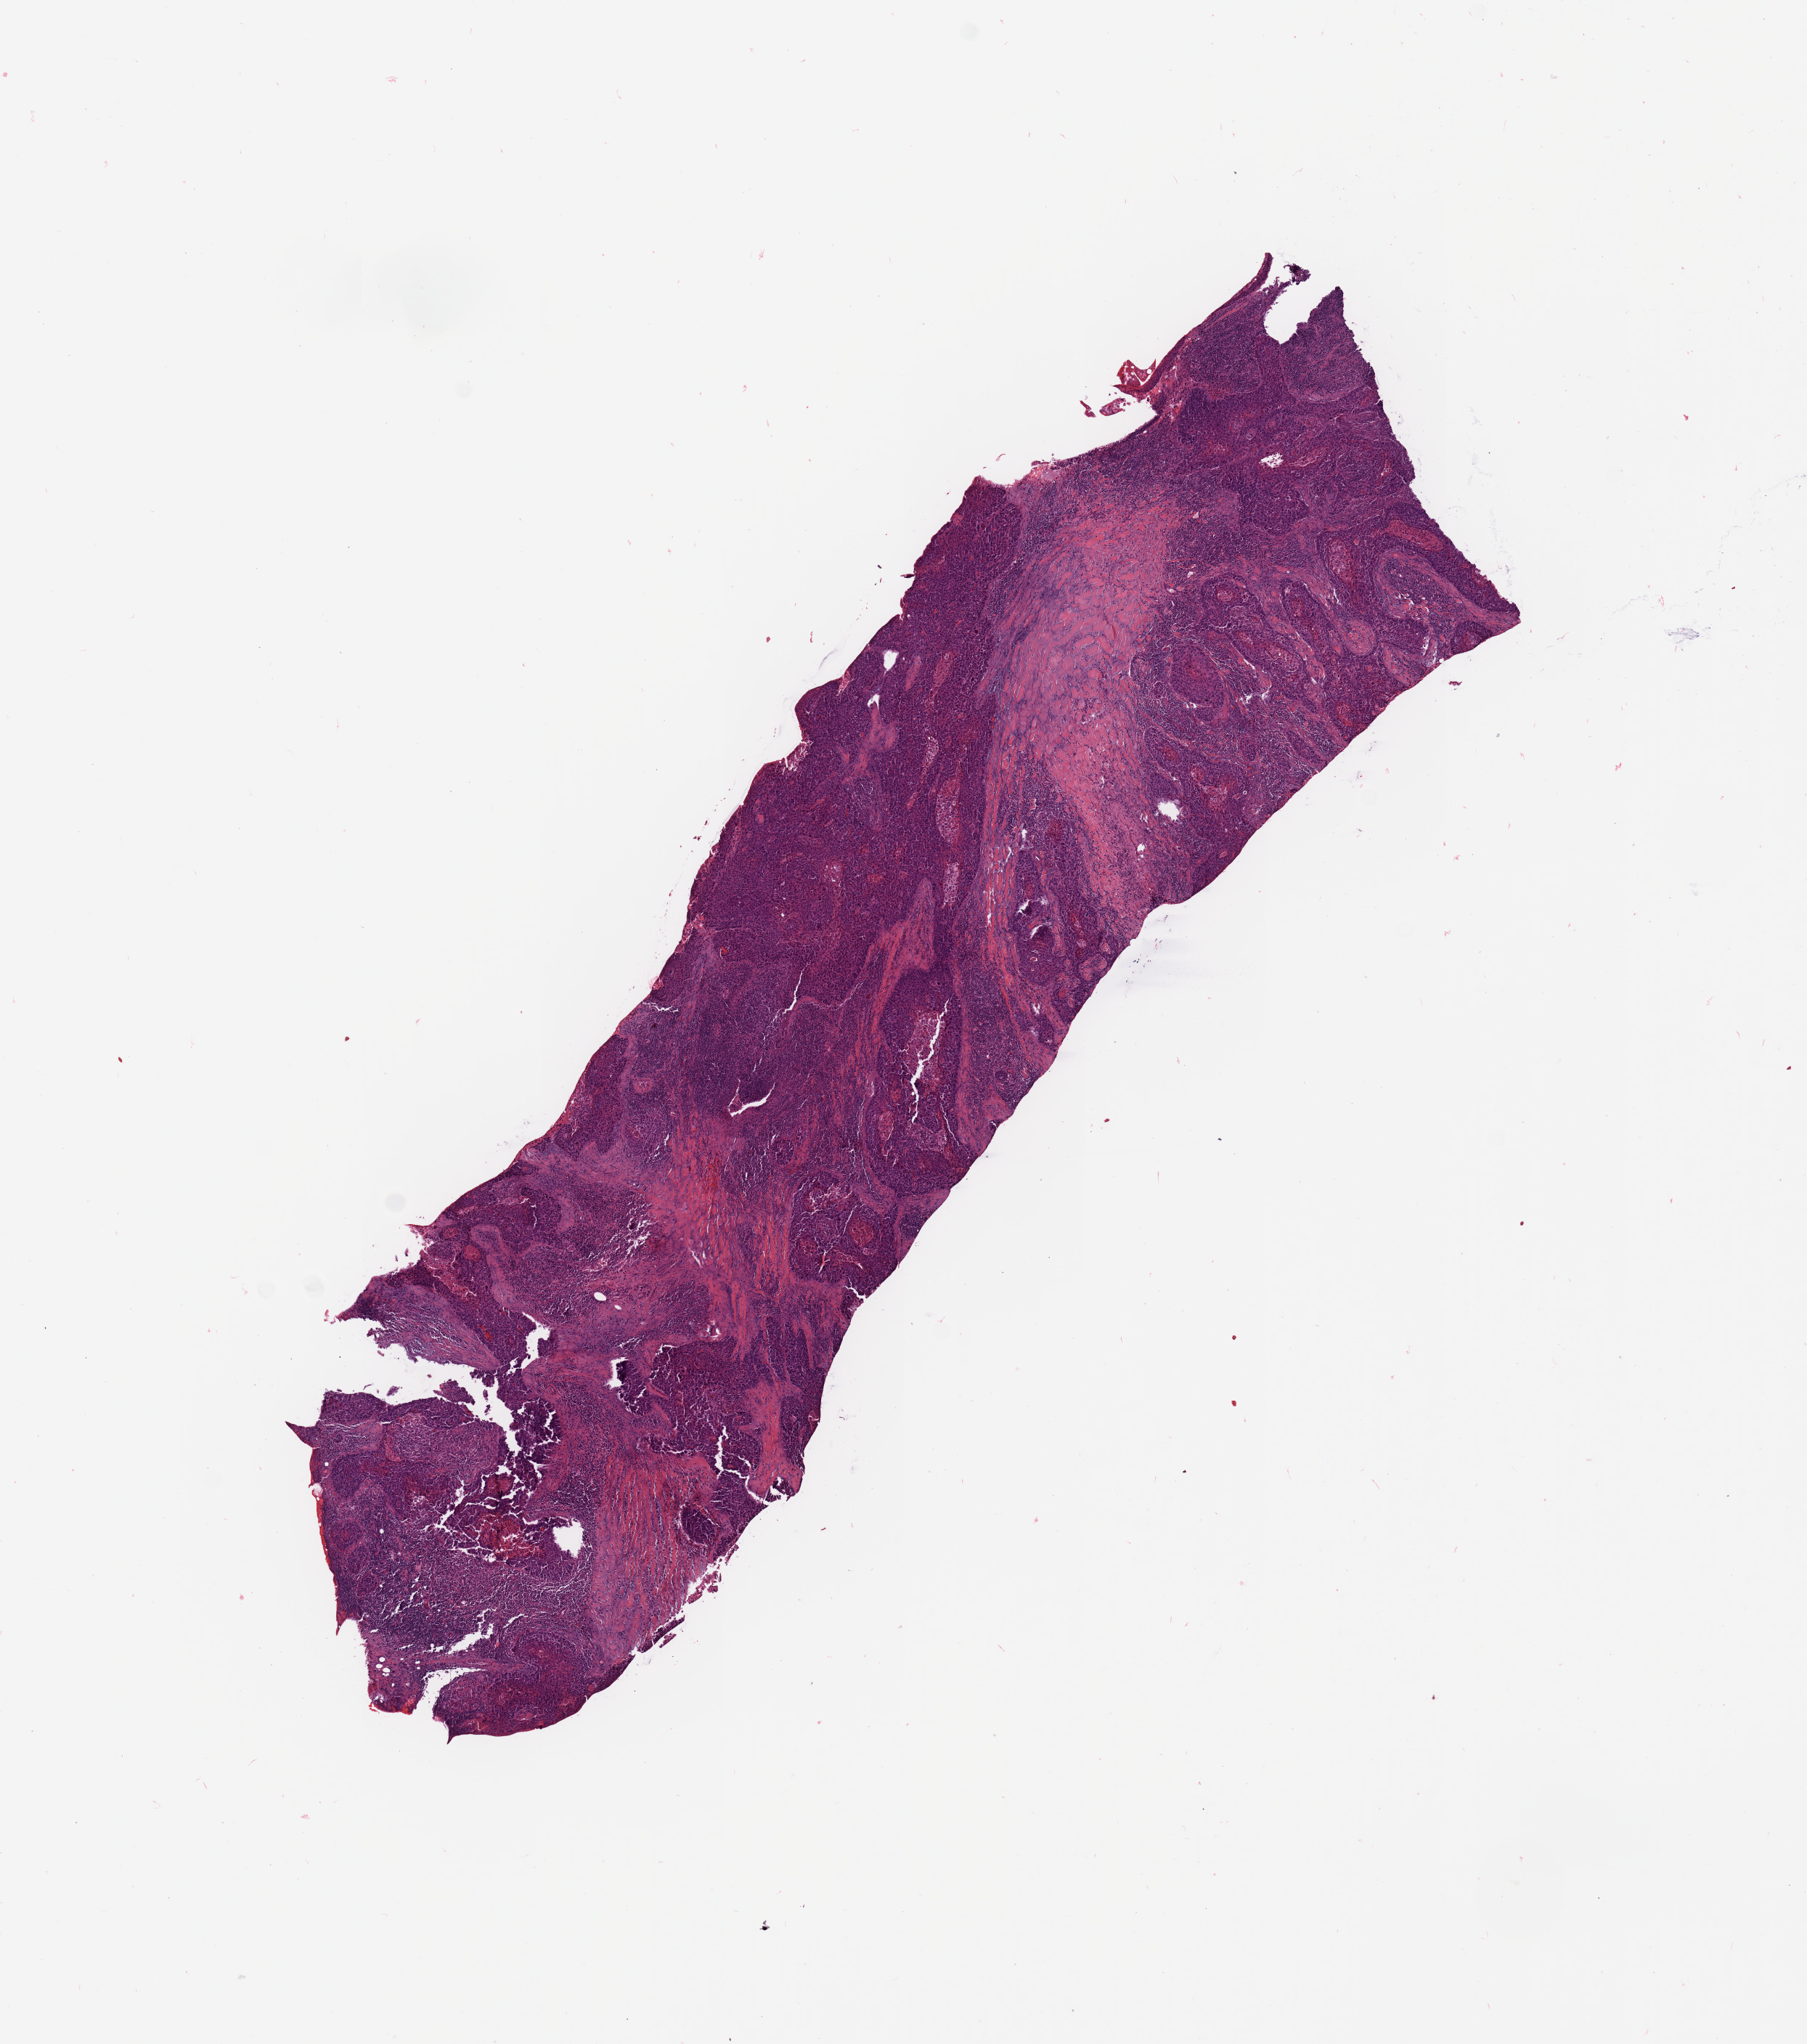
Whole-slide histology image, H&E, low-resolution overview of the scanned area, about 9.8 x 11.1 mm, tumour tissue sample, sampled site: lung. 67-year-old male patient. Histologic grade: G2 (moderately differentiated). Composition of this section per pathologist review: tumour nuclei 80%, necrosis 5%.
AJCC pathologic stage: IIIA. Diagnosis: Squamous cell carcinoma, NOS.